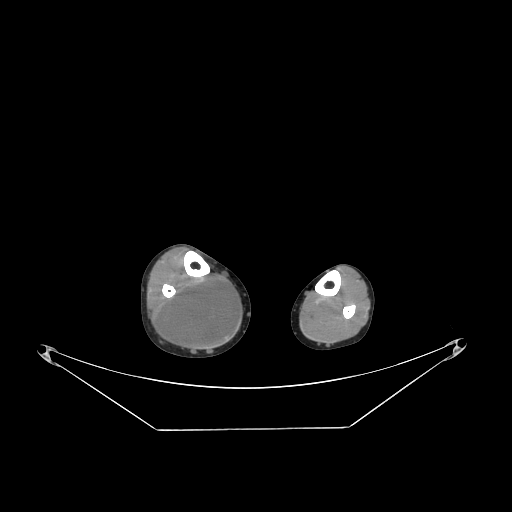
CT of an extremity soft-tissue mass (from a PET/CT study), one axial slice; position 84 of 267 along the scan axis; reconstruction kernel STANDARD; soft-tissue window (W 400 / L 40 HU); 3.75 mm slice thickness; 512 × 512 image matrix, field of view 500 × 500 mm. Male patient. From the clinical record (not read from this slice): histological type: liposarcoma - round cell; grade: high; site of the primary tumour: right calf.
Outlined on this slice (expert contour drawn on MRI and transferred to this co-registered scan by the dataset authors):
- gross tumour volume (mass): bounding box (x1, y1, x2, y2) in pixels: (162, 276, 238, 346)